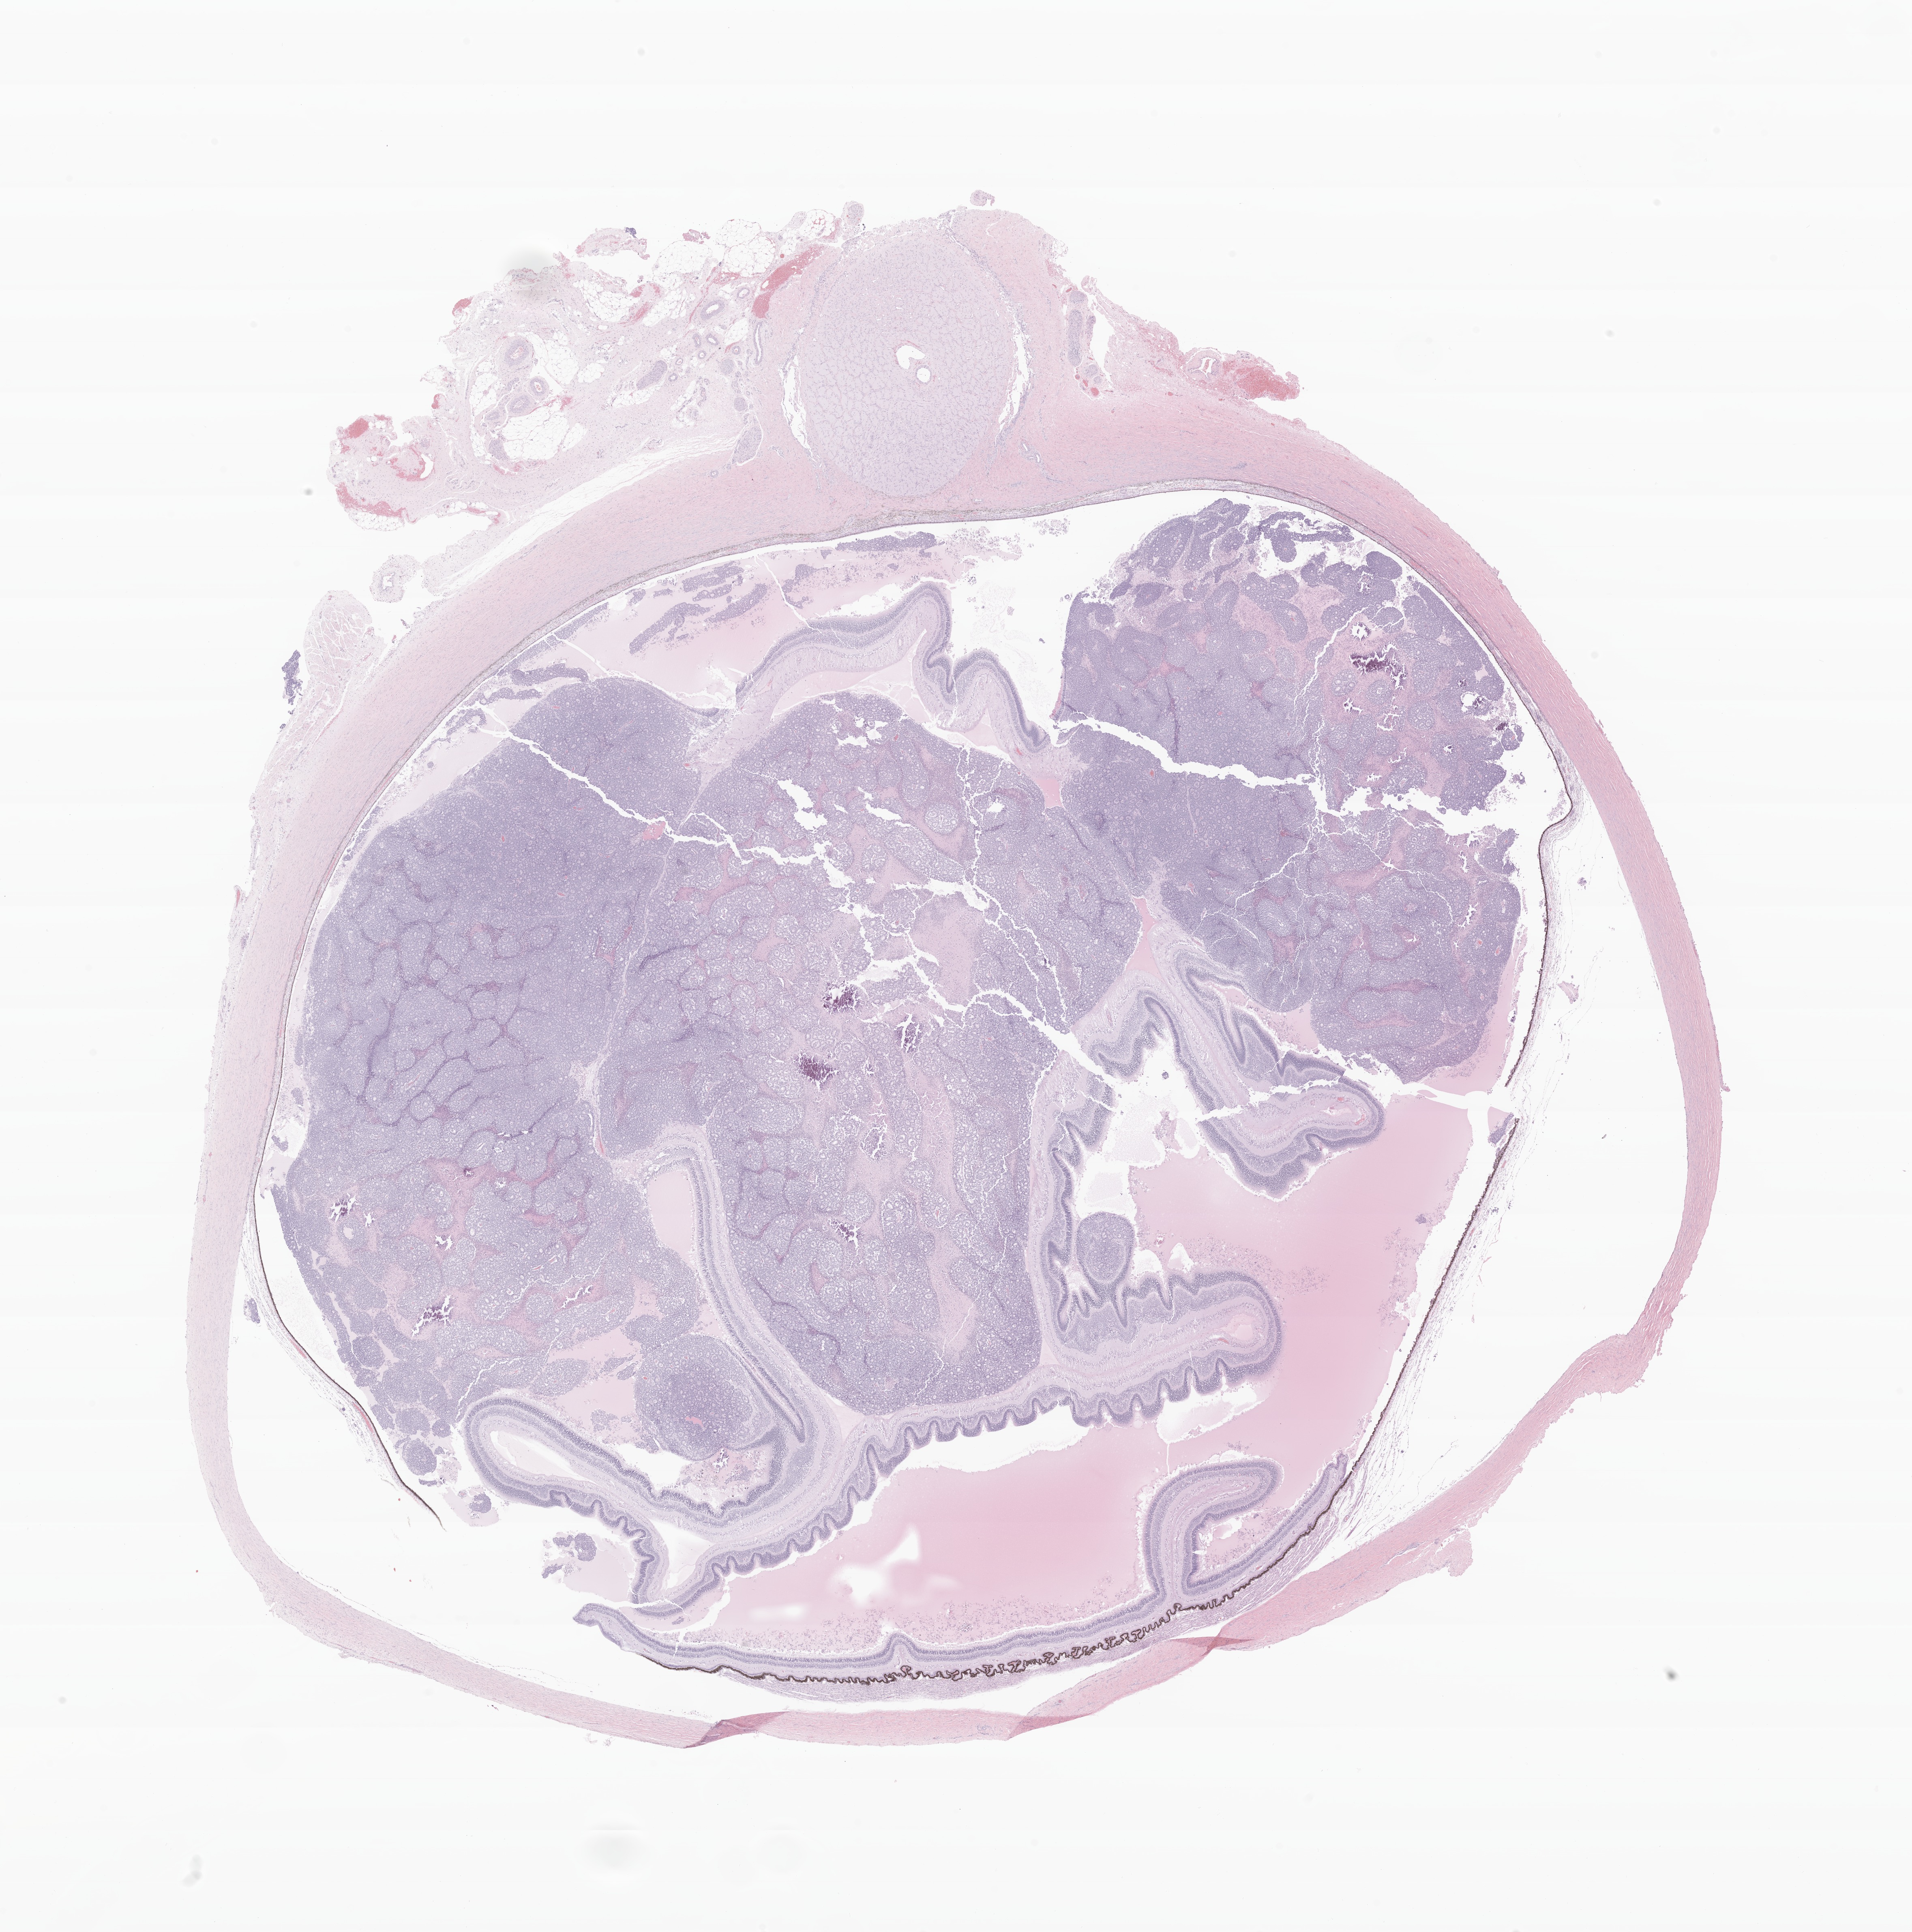
Digitized hematoxylin and eosin (H&E)-stained section of tumor tissue from the eye — a low-resolution overview of the entire scanned area, about 19.8 x 20.0 mm; FFPE section. Female patient, age 70 days.
Diagnosis (ICD-O-3 morphology term): Retinoblastoma, NOS.